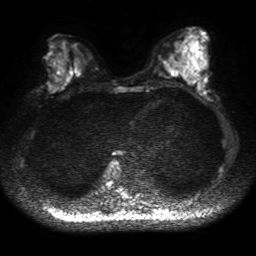
Breast MRI, one axial slice; slice 19 of 50 in the series (ordered by position); diffusion-weighted series; image 2 of 4 stored at this slice position (different b-values; order by instance number); 1.5 T; 4 mm slice thickness; 256 × 256 image matrix, field of view 320 × 320 mm. Female patient.
Annotated regions visible in this slice (expert manual segmentation):
- tumour on diffusion-weighted imaging: bounding box [x1, y1, x2, y2] px = [49, 83, 58, 92]